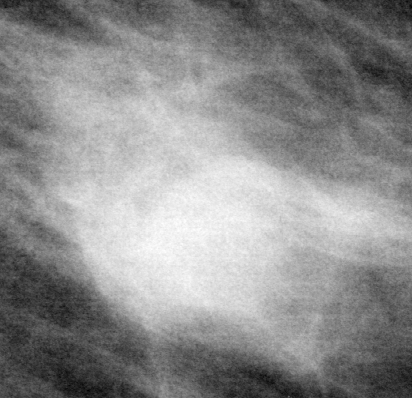
Region of interest cut from a scanned film mammogram (one marked finding), left breast, MLO view.
- Finding: mass, margins ill defined; BI-RADS assessment category 5; pathology (as recorded): malignant.